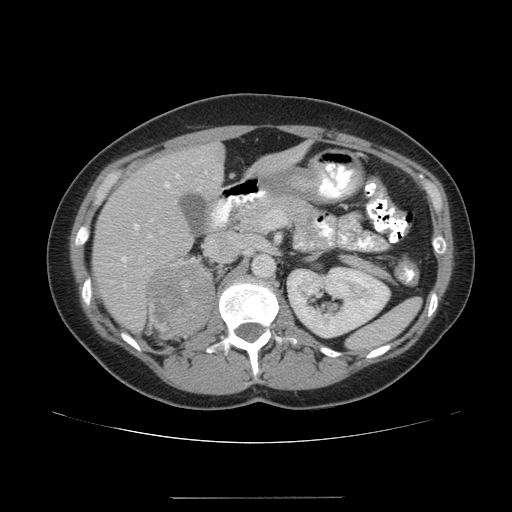
Contrast-enhanced abdominal CT, one axial slice. Position 104 of 161 along the scan axis. Intravenous contrast given. Soft-tissue window (W 400 / L 40 HU). 3.75 mm slice thickness. 512 × 512 image matrix, field of view 380 × 380 mm. Female patient. Case-level facts recorded for this patient, not image findings: diagnosis: adrenocortical carcinoma; tumour side: right adrenal; tumour size at pathology: 9 cm; Ki-67 index: 14 %; stage (as recorded): 3.
Annotated regions visible in this slice (semi-automatic segmentation, software-assisted and operator-edited):
- mass: bounding box <149,261,214,338> (left, top, right, bottom; pixels)